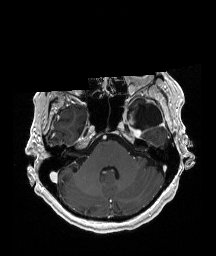
Brain MRI from a brain-tumour surgery series, one axial slice; slice 141 of 192 in the series (ordered by position); T1-weighted post-contrast; 1 mm slice thickness; 216 × 256 image matrix. From the clinical record (not read from this slice): histopathology: Glioblastoma; WHO grade: 4; IDH mutation: no; tumour location: Left Temporal.
Structures marked on this image (outlined manually by an expert reader):
- previous resection cavity: bounding box [x1, y1, x2, y2] px = [135, 104, 162, 130]